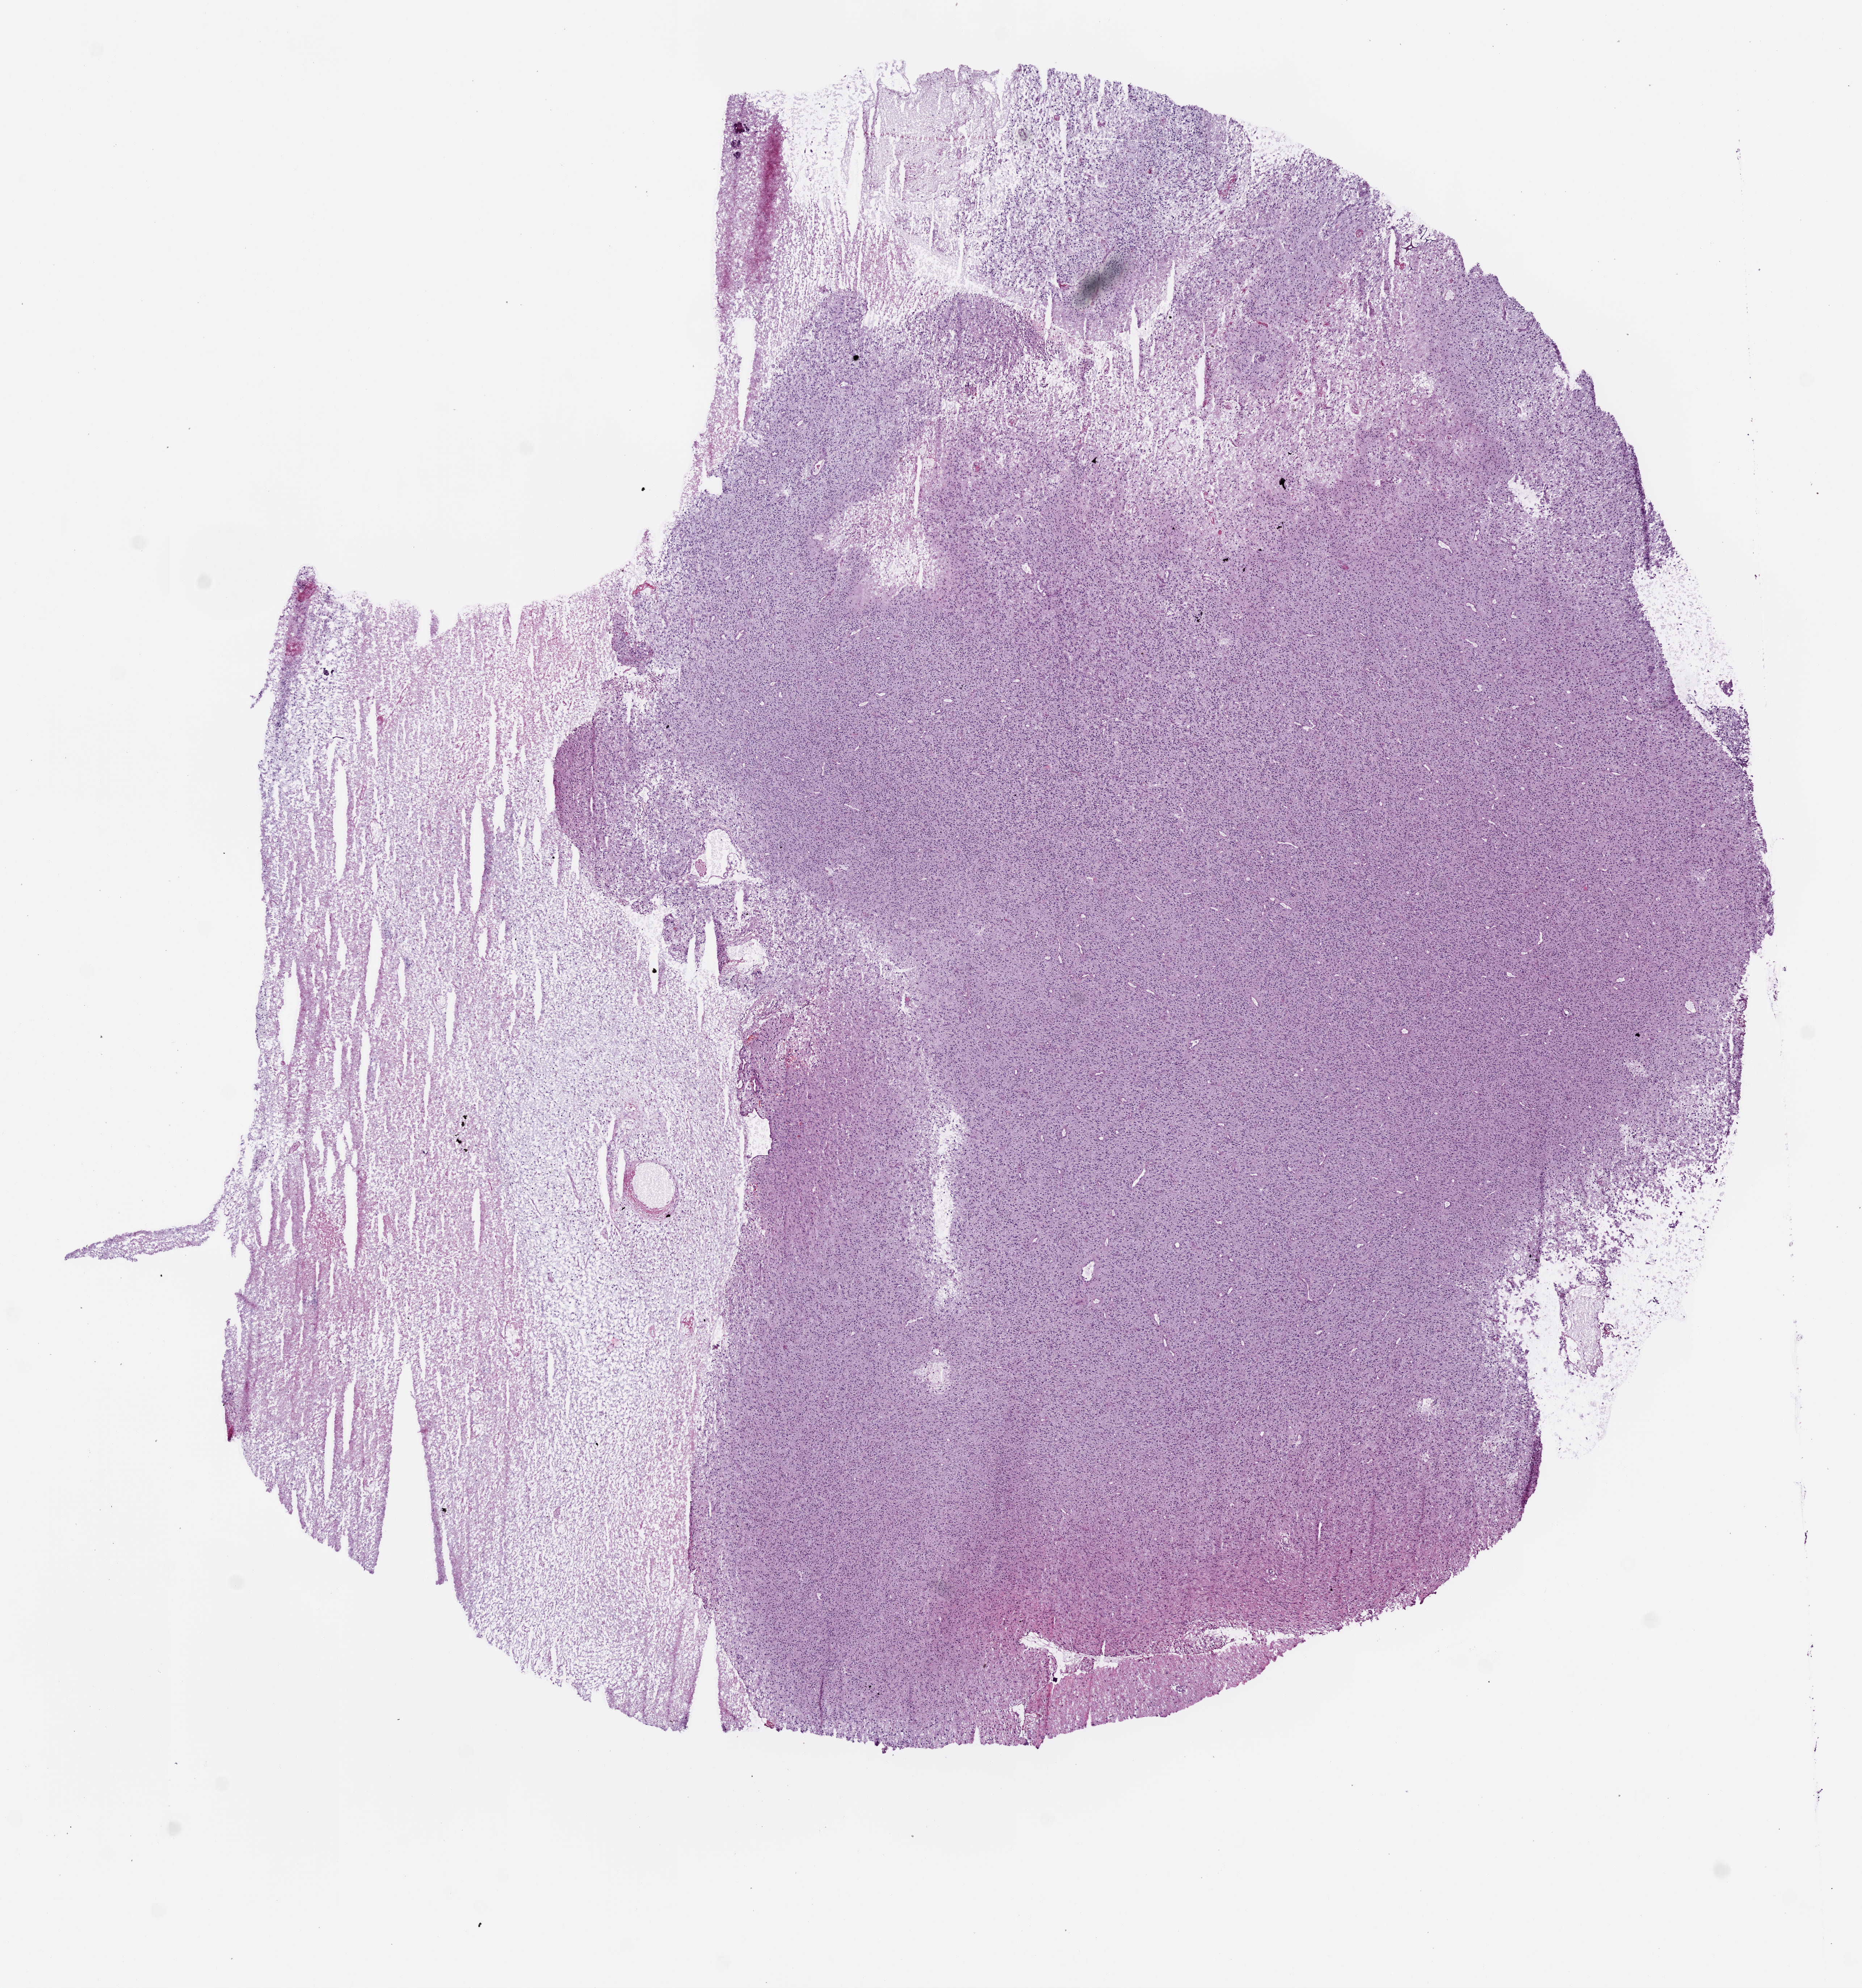
H&E-stained whole-slide image — the whole scanned area (about 10.3 x 11.0 mm) at the scan's own resolution, acquired at 5x, frozen section from the bottom of the tissue portion, sample: primary tumour, brain. Patient: male, age at initial diagnosis 61 years. Composition of this section per pathologist review: tumour cells 100%, tumour nuclei 80%, normal cells 0%, stromal cells 0%, necrosis 0%.
Pathologic diagnosis: Glioblastoma.